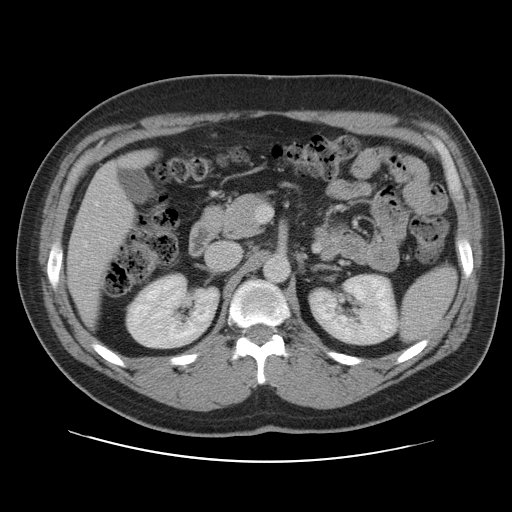
Contrast-enhanced abdominal CT, one axial slice. 120 kVp. Intravenous contrast given. Soft-tissue window (W 400 / L 40 HU). 5 mm slice thickness. 512 × 512 image matrix. Male patient, age 35 years. From the clinical record (not read from this slice): diagnosis: colorectal cancer liver metastases, imaged before liver resection; multiple liver metastases: yes; largest metastasis: 2.8 cm; disease in both lobes: yes.
Outlined on this slice (outlined manually by an expert reader):
- liver: bounding box (x1, y1, x2, y2) in pixels: (68, 152, 156, 324)
- planned liver remnant (the part of the liver to remain after resection): (68, 152, 156, 324)